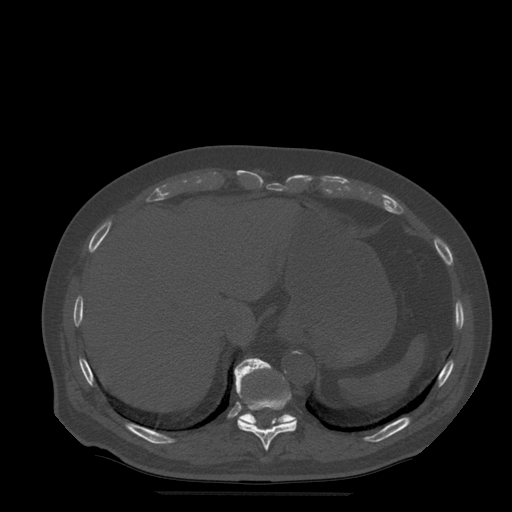
CT including the spine, one axial slice. Slice 261 of 522 in the series (ordered by position). Bone window (W 1800 / L 400 HU). 1.25 mm slice thickness. 512 × 512 image matrix. Patient age 72 years. From the clinical record (not read from this slice): primary cancer: prostate.
Outlined on this slice (semi-automatic segmentation, software-assisted and operator-edited):
- T10 vertebra: box from (x=235, y=367) to (x=297, y=451) px
- T11 vertebra: (x=235, y=358)–(x=297, y=426)